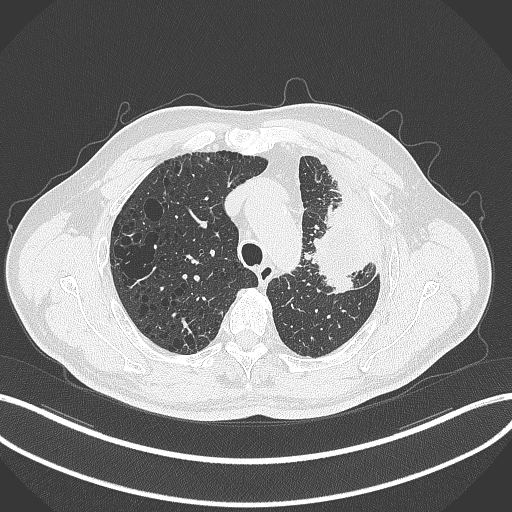
Chest CT, one axial slice. Position 243 of 297 along the scan axis. Reconstruction kernel B70f. Lung window (W 1500 / L -600 HU). 1 mm slice thickness. 512 × 512 image matrix, field of view 400 × 400 mm. Patient: male, 68 years. Case-level facts recorded for this patient, not image findings: clinical TNM (as recorded): T3 N3 M1.
Annotated regions visible in this slice (rectangle marked by the reading radiologist):
- lung tumour (recorded histology: adenocarcinoma): bounding box <310,191,369,300> (left, top, right, bottom; pixels)